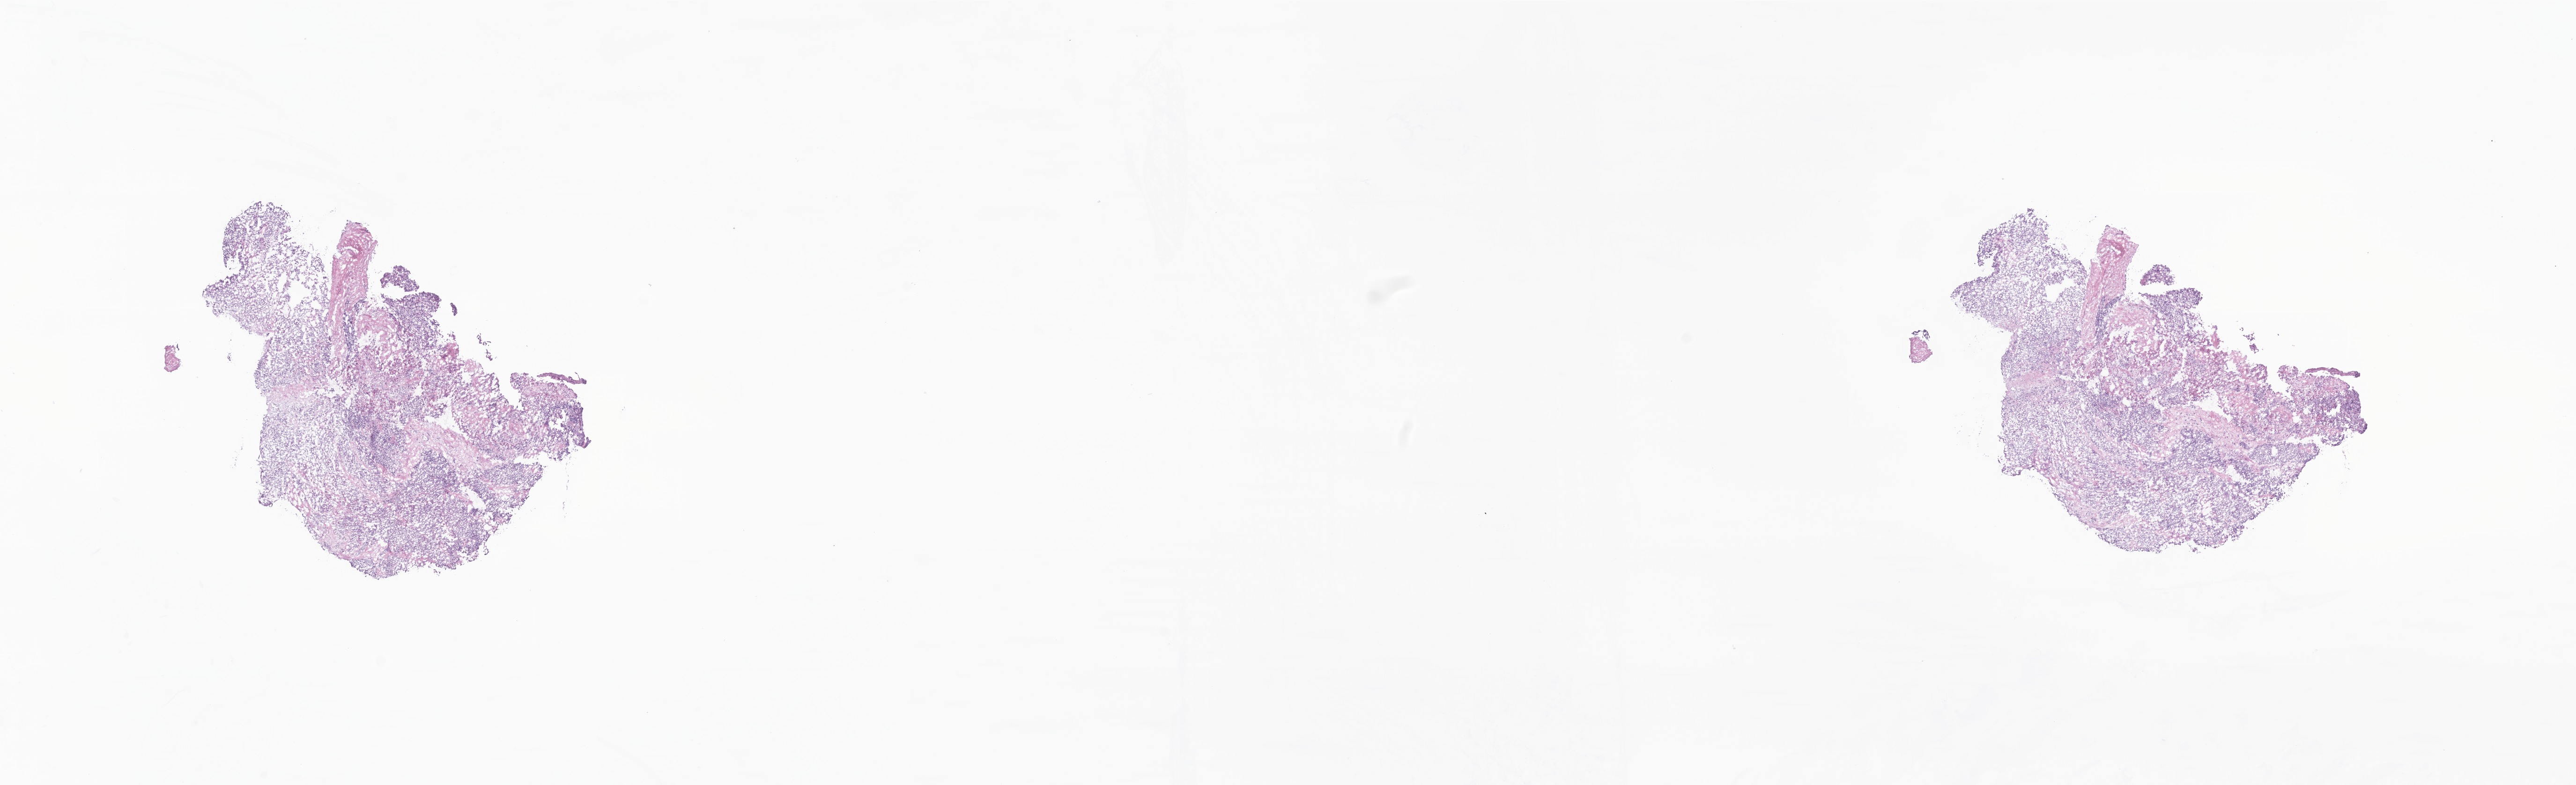
H&E whole-slide image of tumor tissue from the pelvis, shown as a low-resolution overview of the whole scanned area (about 23.2 x 7.1 mm). Frozen section (OCT-embedded). Patient female; age 191 months.
Diagnosis: Alveolar rhabdomyosarcoma.